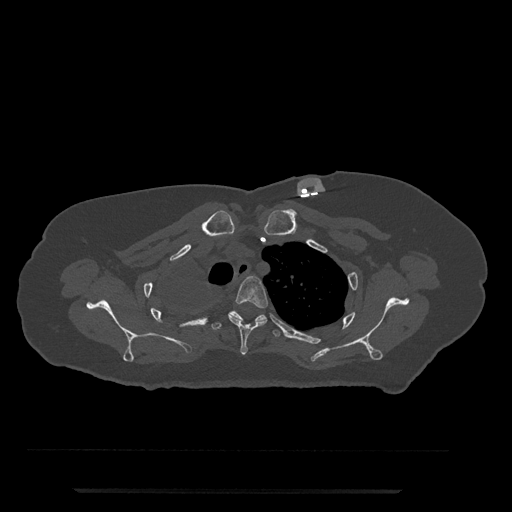
CT including the spine, one axial slice; slice 620 of 797 in the series (ordered by position); reconstruction kernel Br40s/3; 120 kVp; bone window (W 1800 / L 400 HU); 0.5 mm slice thickness; 512 × 512 image matrix. Patient: female, 51 years. Case-level facts recorded for this patient, not image findings: primary cancer: neuro; vertebrae with lytic lesions (as recorded): T8.
Outlined on this slice (semi-automatic segmentation, software-assisted and operator-edited):
- T3 vertebra: box from (x=228, y=276) to (x=269, y=355) px
- T4 vertebra: (x=202, y=310)–(x=285, y=337)